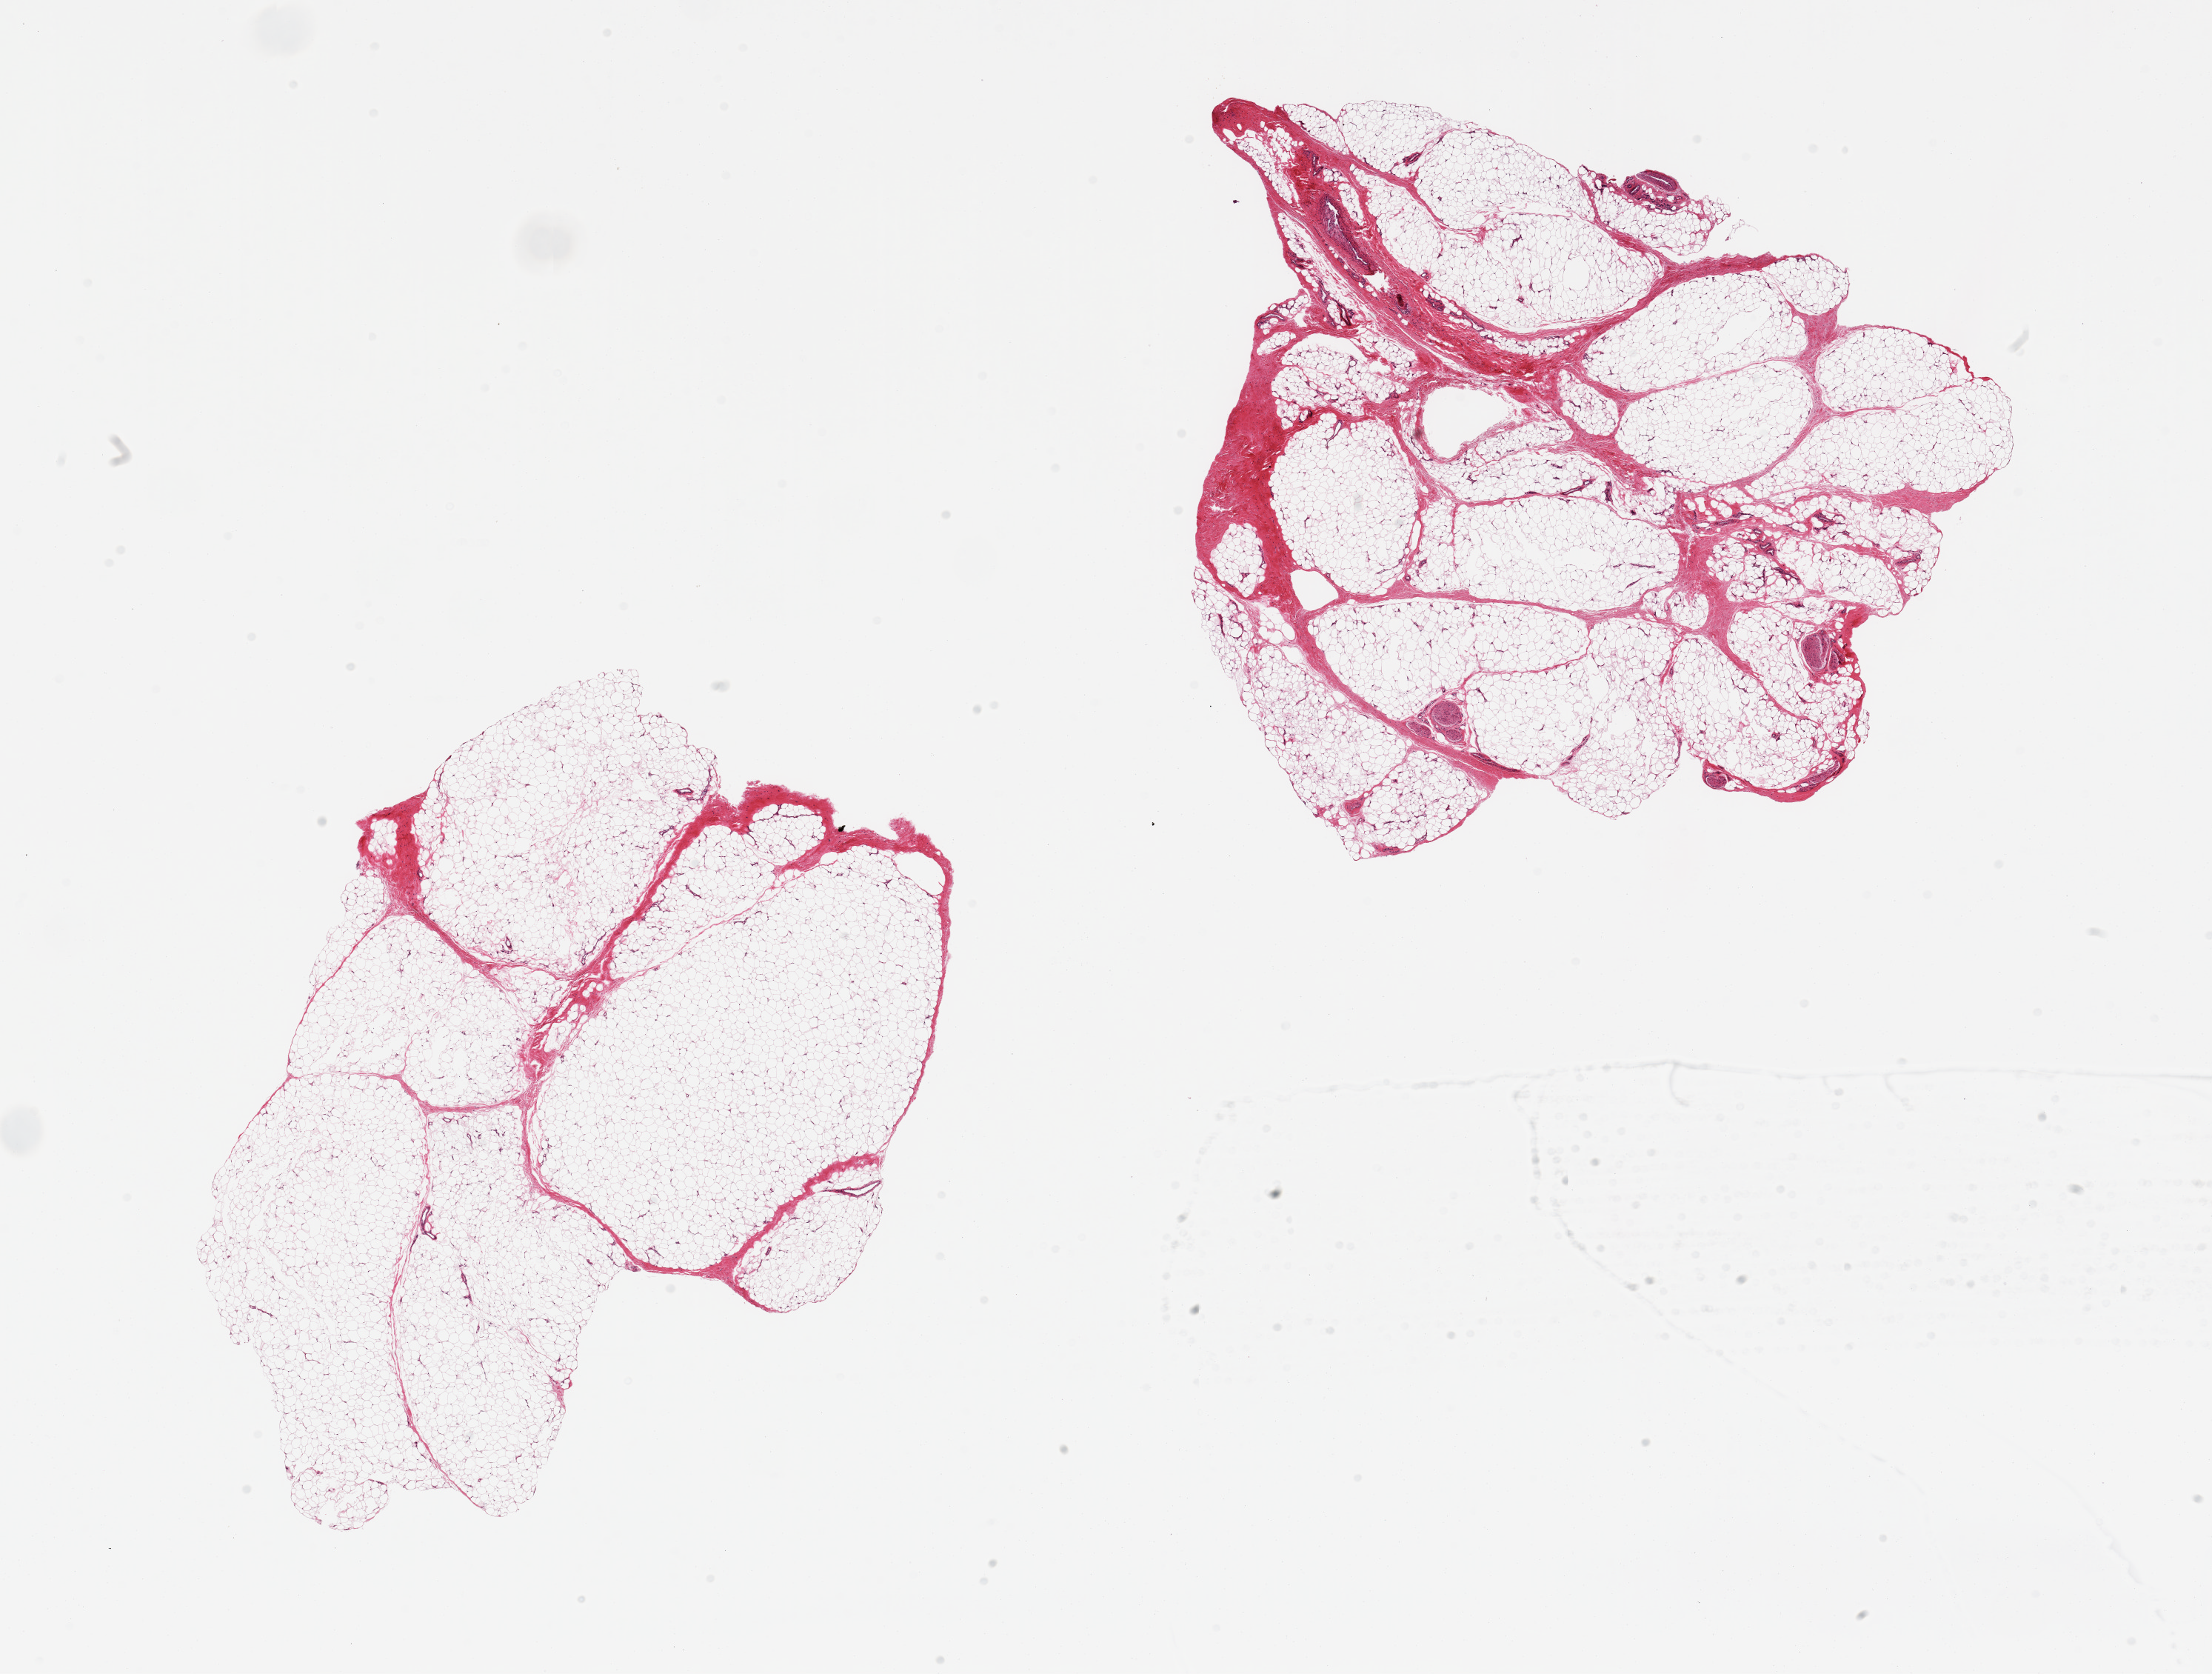
Whole-slide image, H&E stain — low-resolution overview of the scanned area, about 23.6 x 17.9 mm; PAXgene-fixed paraffin-embedded (PFPE) section; section of adipose tissue (target tissue); tissue donor sample. Donor sex: female.
• review note (as recorded): 2 pieces, ~15% fascia/vascular tissue